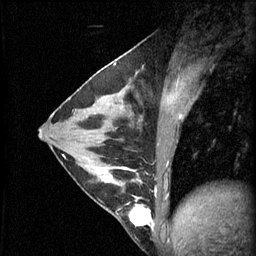
Breast MRI (dynamic contrast-enhanced), one sagittal slice; slice 27 of 60 in the series (ordered by position); 3 images stored at this slice position (order not interpretable as contrast timing); 1.5 T; TE 4.2 ms, TR 11 ms; 256 × 256 image matrix, field of view 180 × 180 mm. Patient: female, 29 years.
Annotated regions visible in this slice (semi-automatic segmentation, software-assisted and operator-edited):
- analysis volume of interest (the breast-tissue region the enhancement analysis was run in; not a lesion): box from (x=93, y=164) to (x=153, y=229) px
- tumour enhancement mask (voxels above the 70 % enhancement threshold inside the analysis volume of interest): (x=93, y=168)–(x=153, y=229)